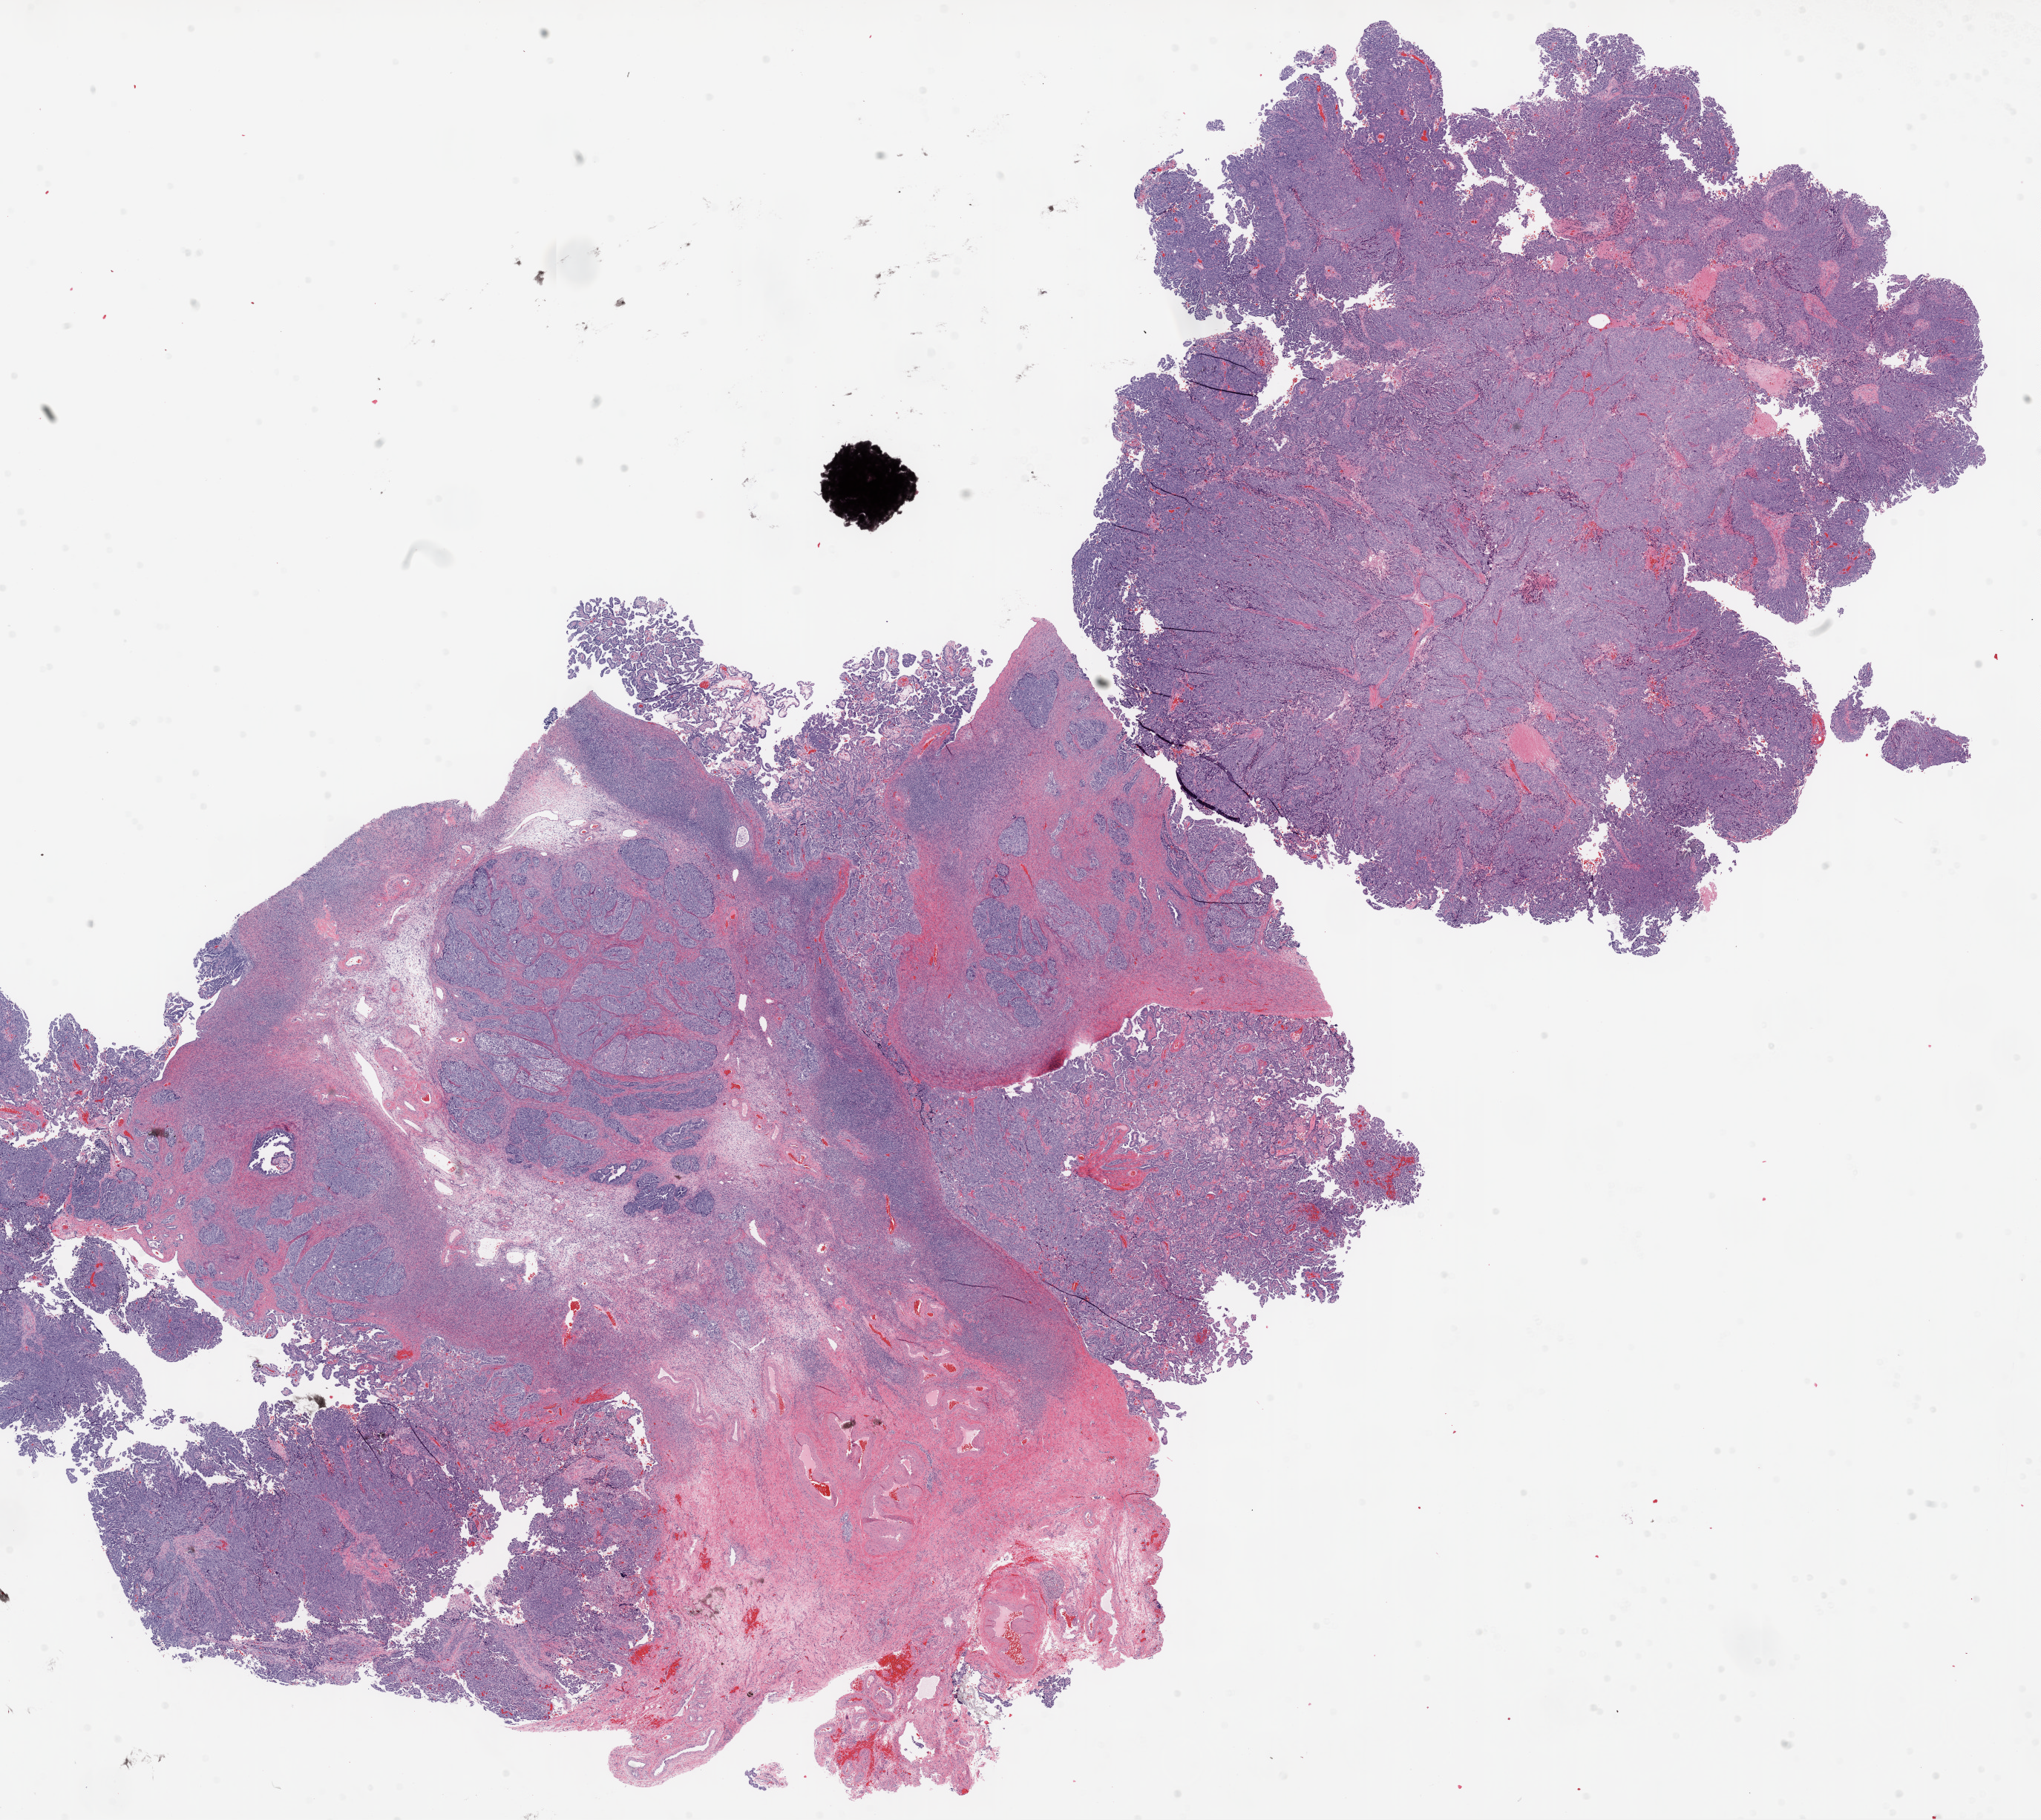
Digitized H&E tissue section (whole slide), low-resolution overview of the scanned area, about 22.1 x 19.7 mm; frozen section from the top of the tissue portion; ovary, primary tumour sample. Patient: female, age at initial diagnosis 57 years. Histologic grade: G3 (poorly differentiated). Pathologist review of this section (percent, as recorded): tumour cells 75%, tumour nuclei 75%, normal cells 15%, stromal cells 10%, necrosis 3%.
Pathologic diagnosis: Serous cystadenocarcinoma, NOS. FIGO stage: IIIC.